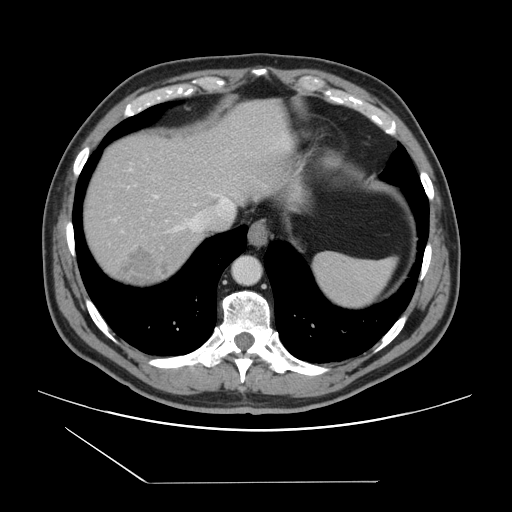
Contrast-enhanced abdominal CT, one axial slice. Slice 126 of 157 in the series (ordered by position). Soft-tissue window (W 400 / L 40 HU). 512 × 512 image matrix, field of view 407 × 407 mm. Male patient, age 61 years. Case-level facts recorded for this patient, not image findings: diagnosis: colorectal cancer liver metastases, imaged before liver resection; multiple liver metastases: yes; largest metastasis: 5.5 cm.
Outlined on this slice (manually delineated by an expert):
- hepatic veins: bounding box <154,195,234,233> (left, top, right, bottom; pixels)
- liver: <83,101,295,288>
- planned liver remnant (the part of the liver to remain after resection): <83,116,232,230>
- liver metastasis: <114,246,172,285>